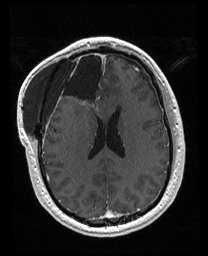
Brain MRI from a brain-tumour surgery series, one axial slice; slice 74 of 176 in the series (ordered by position); T1-weighted post-contrast; 1 mm slice thickness; 208 × 256 image matrix. From the clinical record (not read from this slice): histopathology: Astrocytoma; WHO grade: 4; IDH mutation: yes; tumour location: Right Orbitofrontal Anterior Temporal Insular.
Outlined on this slice (outlined manually by an expert reader):
- previous resection cavity: bounding box (x1, y1, x2, y2) in pixels: (56, 52, 106, 111)